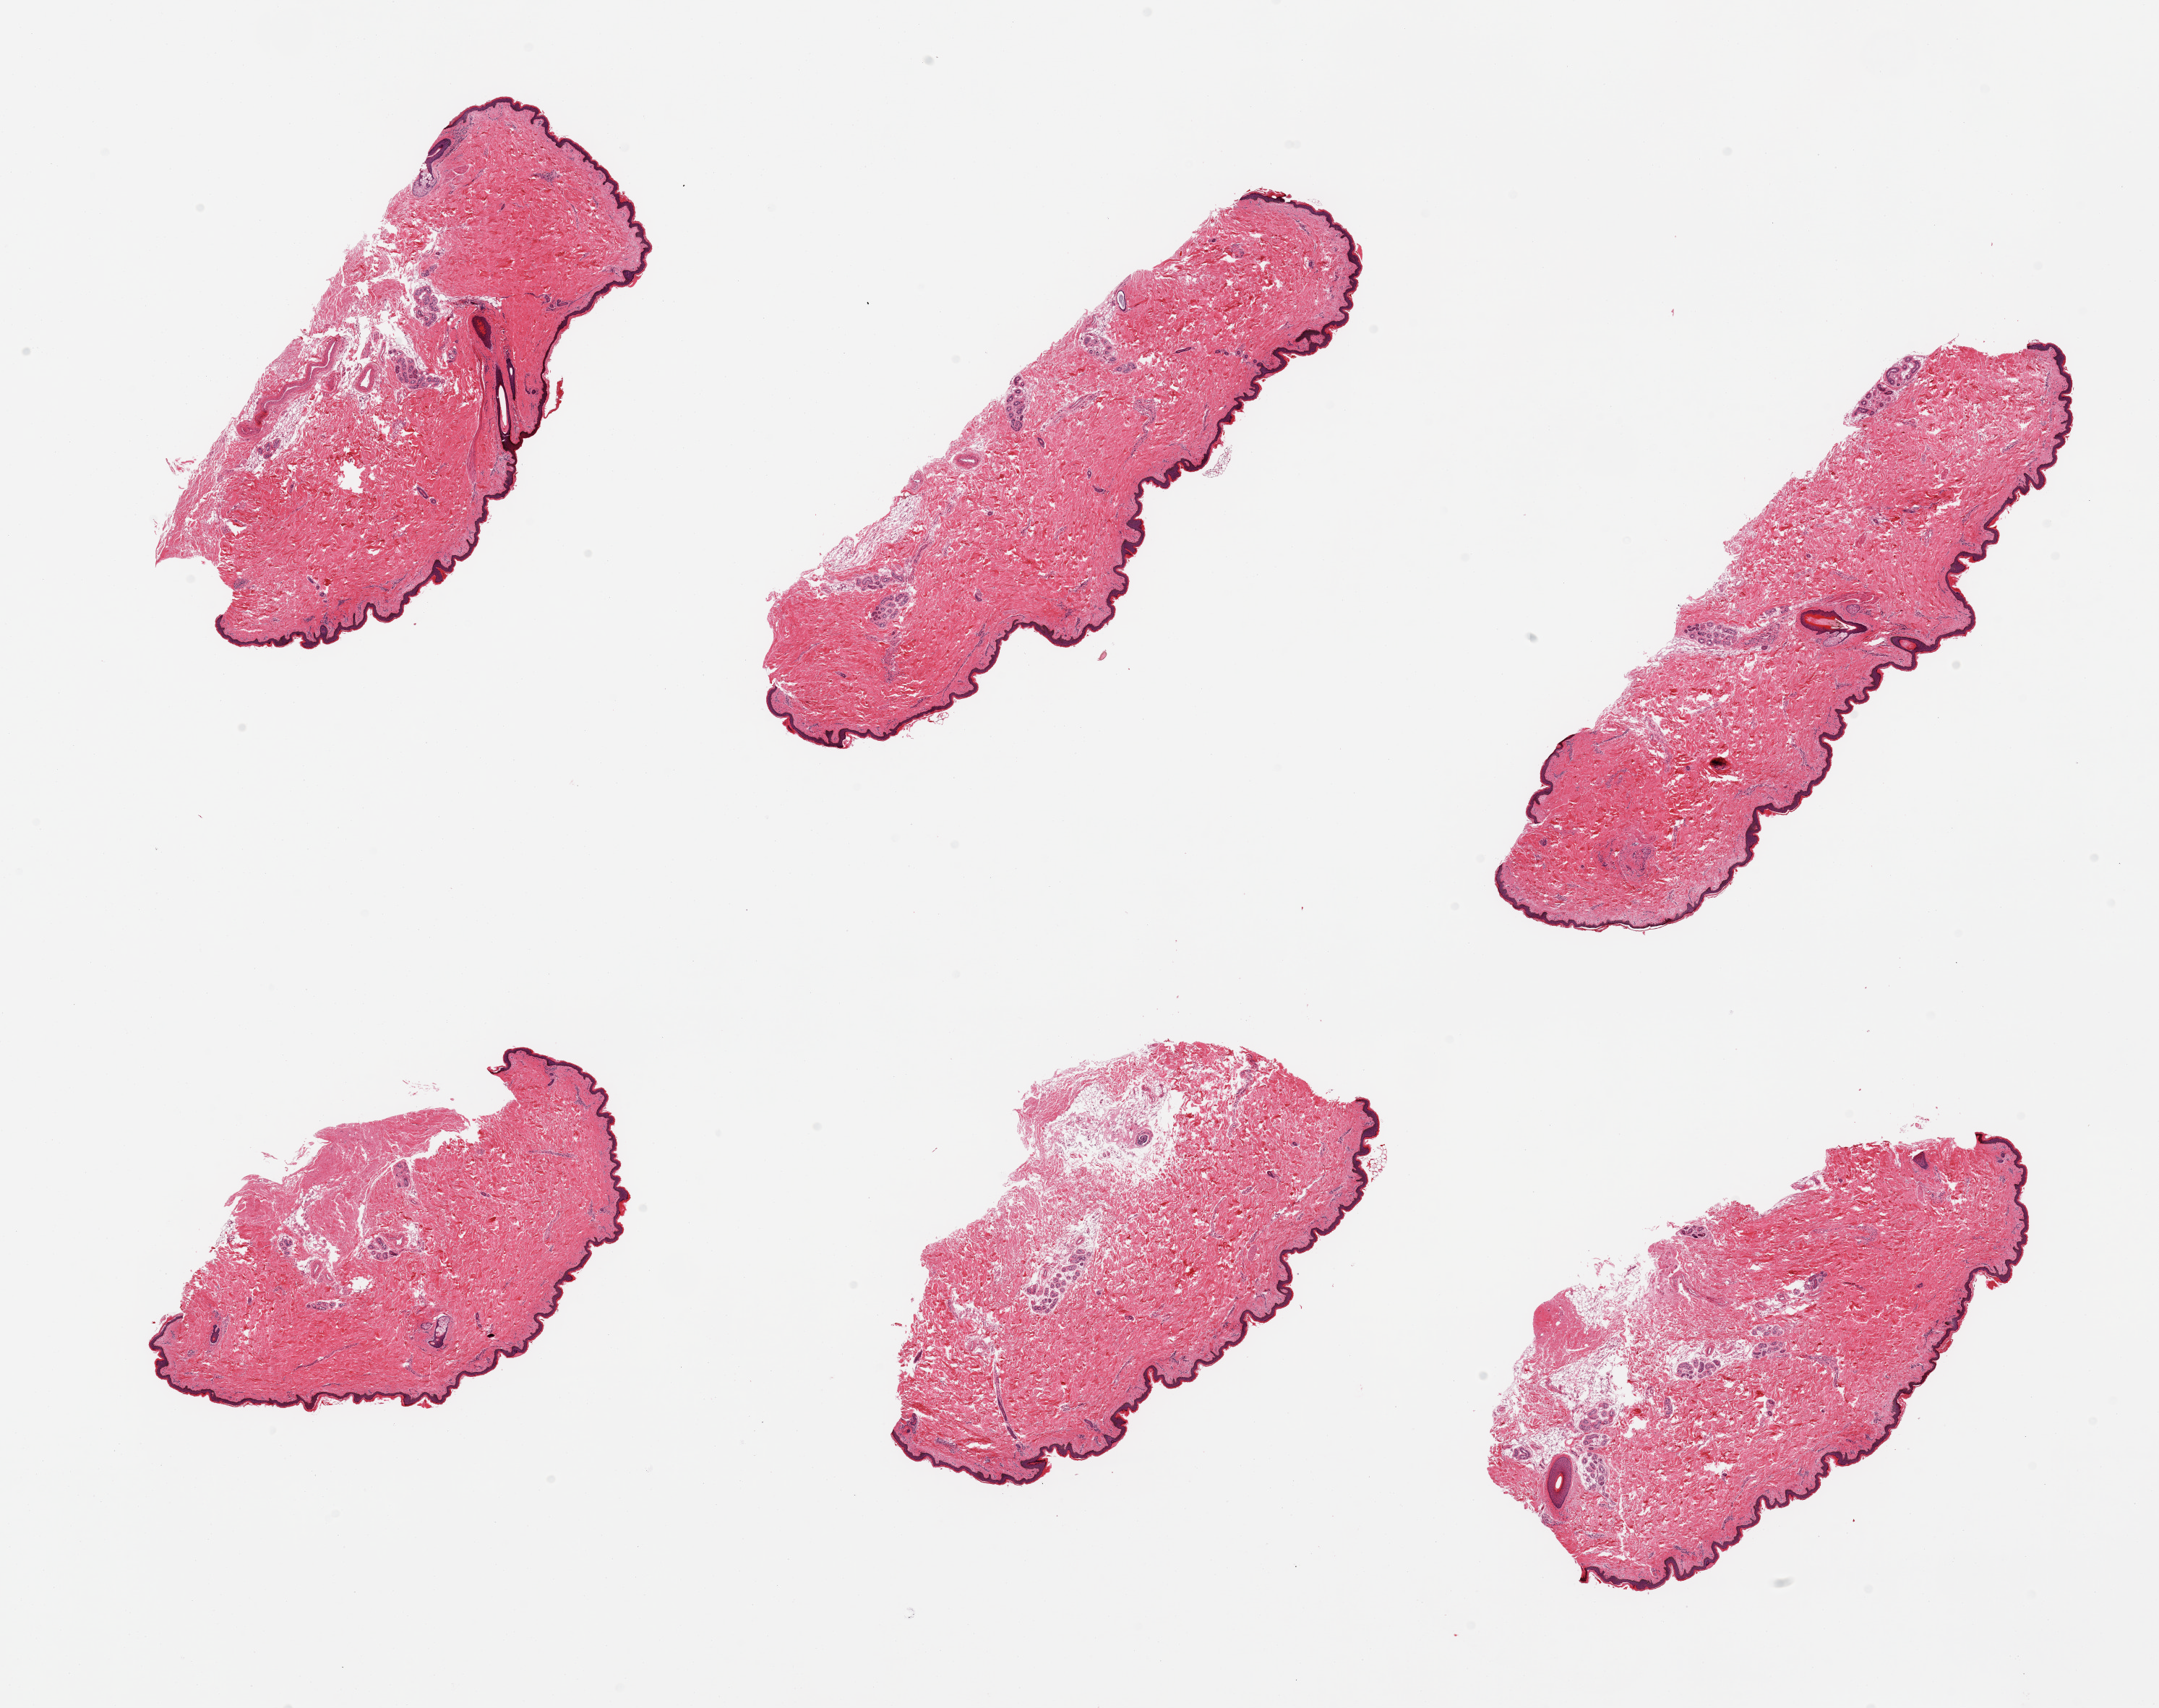
Hematoxylin and eosin (H&E) whole-slide image, brightfield, a low-resolution overview of the entire scanned area, about 23.6 x 18.7 mm (slide scanned at 20x), PAXgene-fixed paraffin-embedded (PFPE) section, section of skin of suprapubic region (target tissue), donor tissue sample.
Pathologist's review note for this sample: 6 pieces, minimal dermal fat; squamous epithelium is ~50-60microns.